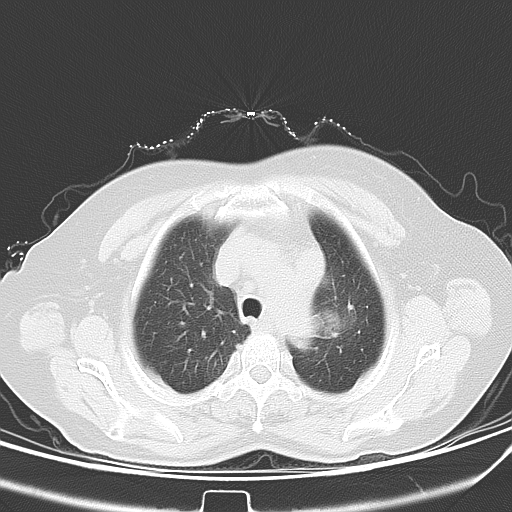
Chest CT, one axial slice. Lung window (W 1500 / L -600 HU). 5 mm slice thickness. 512 × 512 image matrix, field of view 331 × 331 mm. Female patient, age 59 years. From the clinical record (not read from this slice): clinical TNM (as recorded): T3 N1 M0.
Outlined on this slice (bounding box drawn by a radiologist):
- lung tumour (recorded histology: small cell carcinoma): bounding box <310,300,352,345> (left, top, right, bottom; pixels)